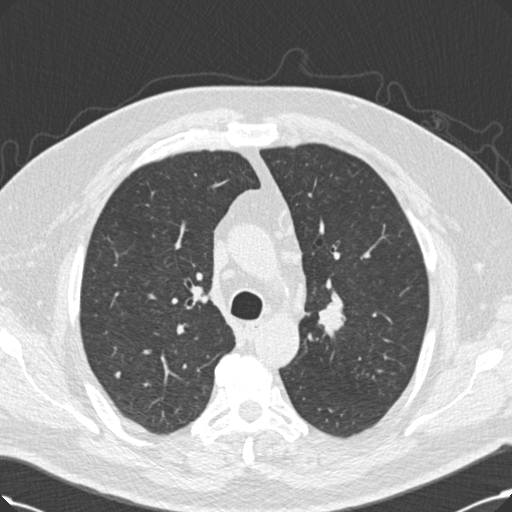
Low-dose screening chest CT, axial slice; third annual screen; lung window (W 1500 / L -600 HU); 2 mm slice thickness; slice 60 of 214 in the series; 512 × 512 image matrix. Male, age 60 years at enrolment. Current smoker at enrolment.
Lesion marked by an expert reader, box from (x=317, y=295) to (x=348, y=329) px. The exam's reader record, not a measurement of the box and not confirmed to be the same lesion: non-calcified nodule or mass ≥4 mm, left upper lobe, 20 × 20 mm, smooth margins, soft tissue attenuation, pre-existing on the prior screen: no. Lung cancer was diagnosed 53 days after this screen: squamous cell carcinoma, NOS, right upper lobe, 27 mm at pathology.